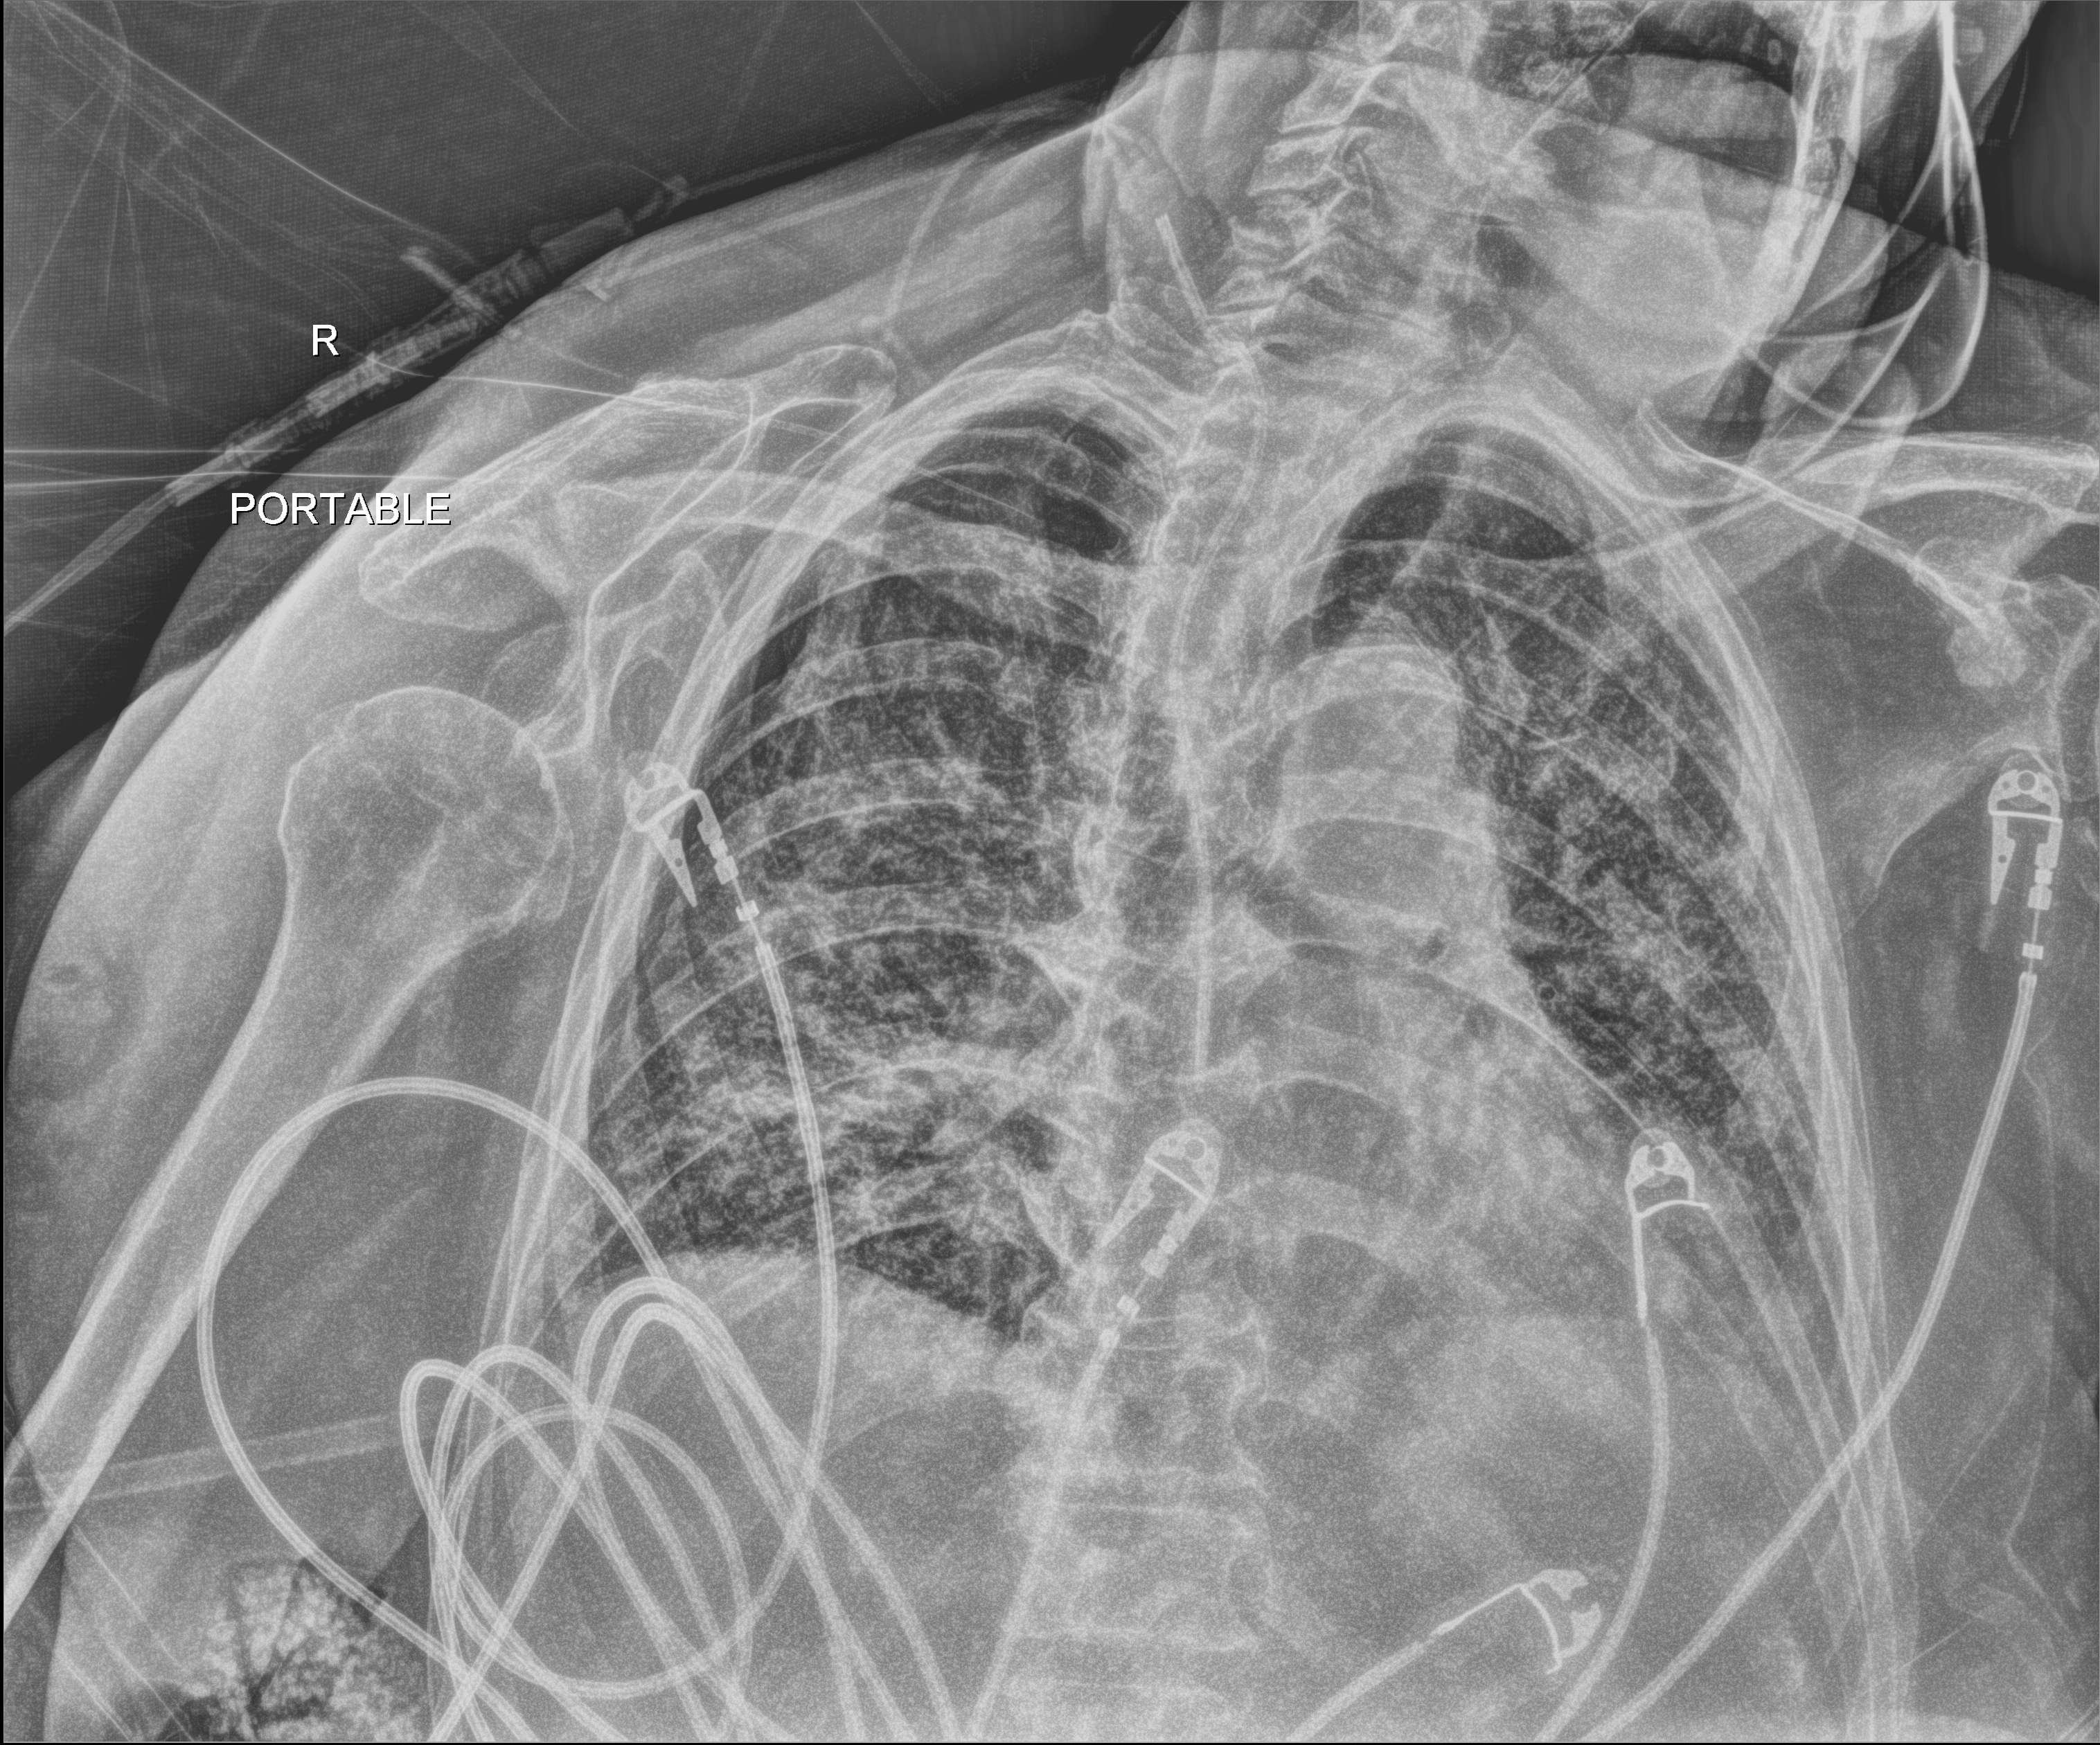
Portable chest radiograph; anteroposterior (AP) projection. Female patient hospitalised with COVID-19, age 75–90 years.
From the hospital-stay record, not from the radiograph (when in the stay this image was taken is not recorded): other chronic lung disease (admission record): no; hypertension (admission record): no.